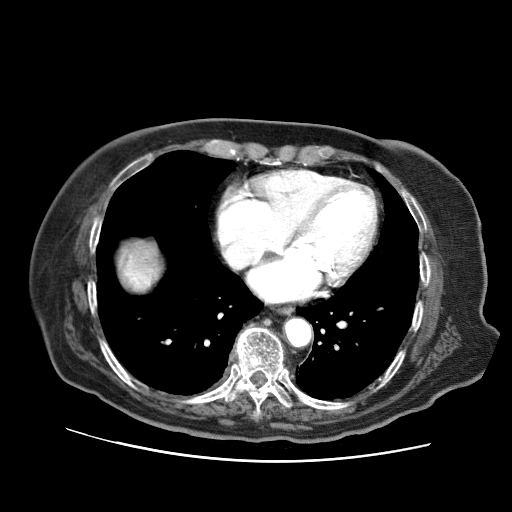
Contrast-enhanced abdominal CT (liver protocol), one axial slice. Soft-tissue window (W 400 / L 40 HU). 2.5 mm slice thickness. 512 × 512 image matrix. Case-level facts recorded for this patient, not image findings: diagnosis: hepatocellular carcinoma (patient treated with transarterial chemoembolisation; whether this scan precedes or follows treatment is not stated here); TNM stage (as recorded): Stage-I; Child-Pugh class: A; tumour differentiation: well differentiated; tumour nodularity: uninodular.
Annotated regions visible in this slice (semi-automatically segmented with operator editing):
- abdominal aorta: bounding box (x1, y1, x2, y2) in pixels: (284, 318, 311, 346)
- liver parenchyma outside the tumour (the mass and vessels are separate outlines, so this box may not span the whole liver): (122, 244, 158, 290)
- liver vessels: (127, 272, 150, 284)